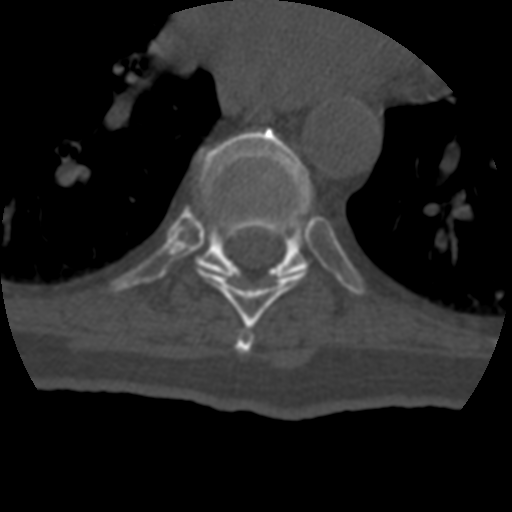
CT including the spine, one axial slice; slice 251 of 399 in the series (ordered by position); reconstruction kernel STANDARD; bone window (W 1800 / L 400 HU); 512 × 512 image matrix, field of view 160 × 160 mm. Patient age 69 years. From the clinical record (not read from this slice): primary cancer: prostate.
Outlined on this slice (semi-automatically segmented with operator editing):
- T7 vertebra: bounding box (x1, y1, x2, y2) in pixels: (235, 329, 254, 354)
- T8 vertebra: (198, 266, 306, 328)
- T9 vertebra: (196, 128, 313, 278)